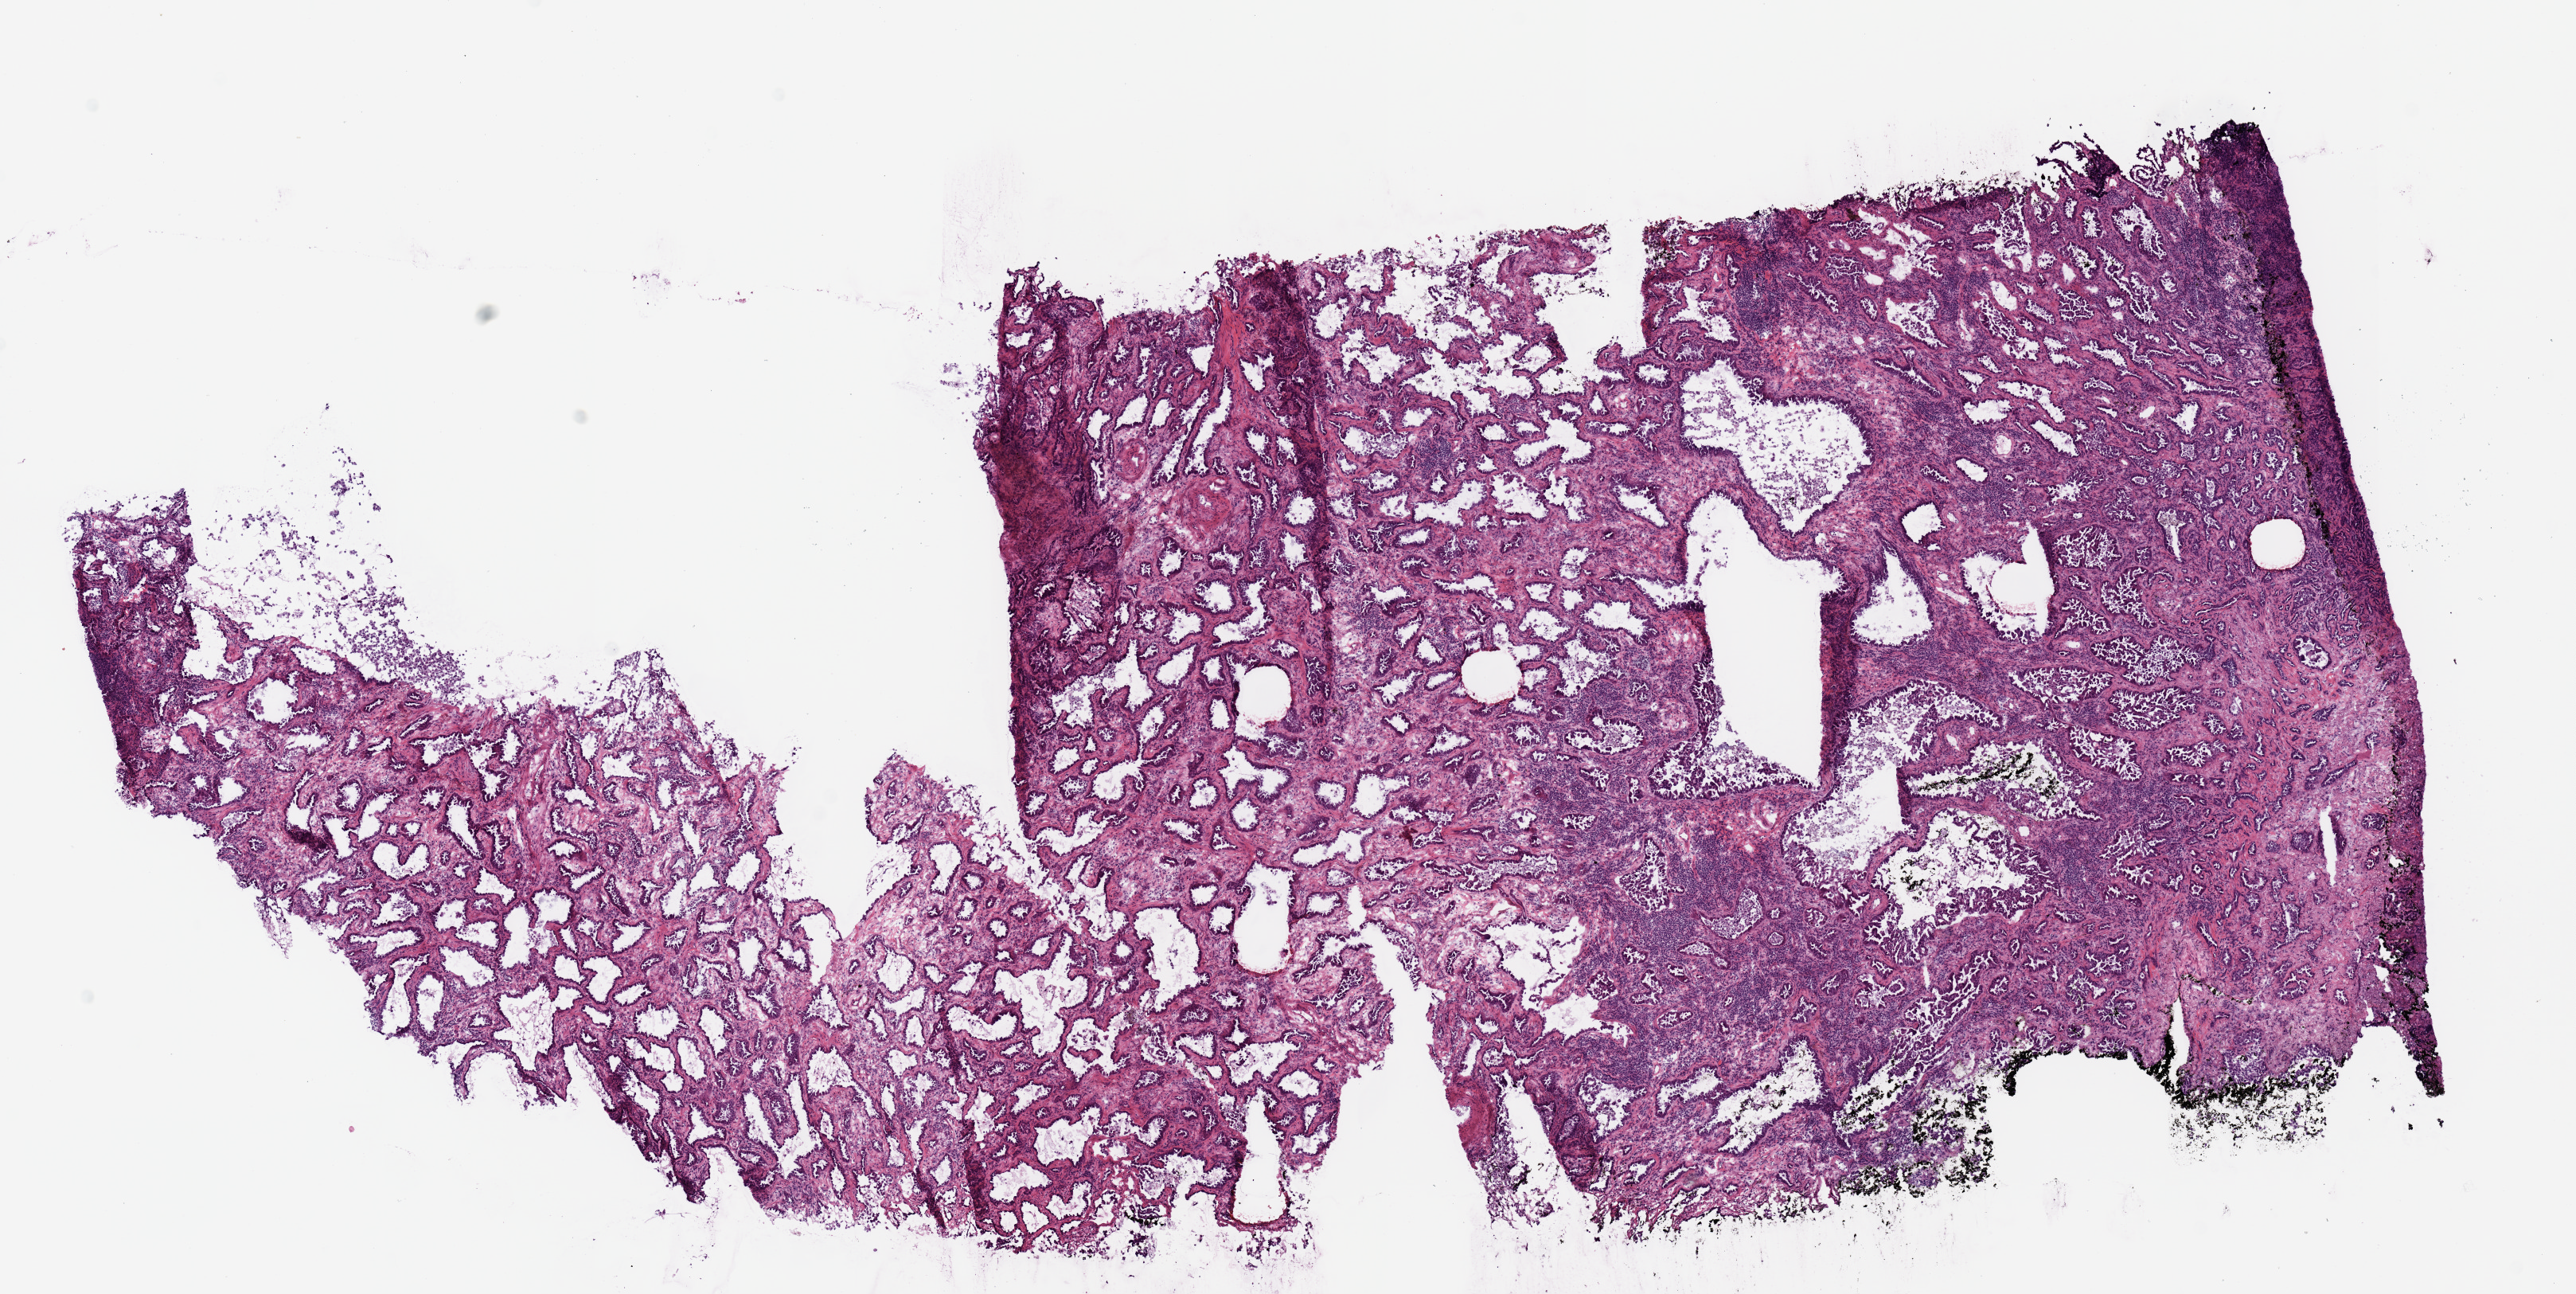
H&E-stained whole-slide image, a low-resolution overview of the entire scanned area, about 12.8 x 6.4 mm (from a 20x scan). Frozen section from the top of the tissue portion. Lung, primary tumour sample. Male, age 71 years at initial diagnosis. Pathologist review of this section (percent, as recorded): tumour cells 70%, tumour nuclei 65%, normal cells 0%, stromal cells 30%, necrosis 0%. Inflammatory infiltration, as recorded: lymphocyte infiltration 0%, monocyte infiltration 0%, neutrophil infiltration 0%.
• AJCC pathologic stage: IA (7th edition)
• laterality: right
• pathologic diagnosis: Adenocarcinoma, NOS